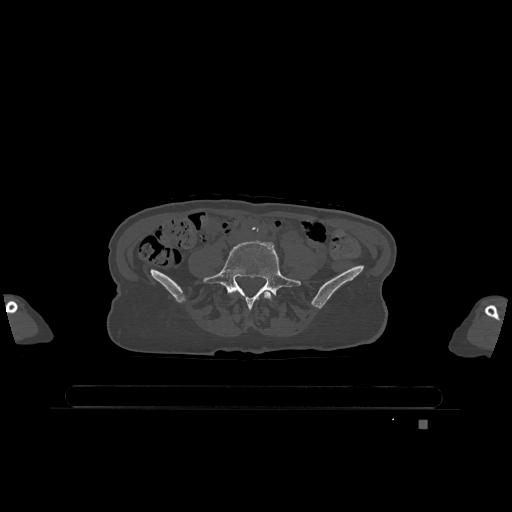
CT including the spine, one axial slice; bone window (W 1800 / L 400 HU); 0.5 mm slice thickness; 512 × 512 image matrix. Female patient, age 74 years. From the clinical record (not read from this slice): primary cancer: lung.
Structures marked on this image (semi-automatic segmentation, software-assisted and operator-edited):
- L4 vertebra: bounding box <263,291,272,300> (left, top, right, bottom; pixels)
- L5 vertebra: <204,241,301,308>